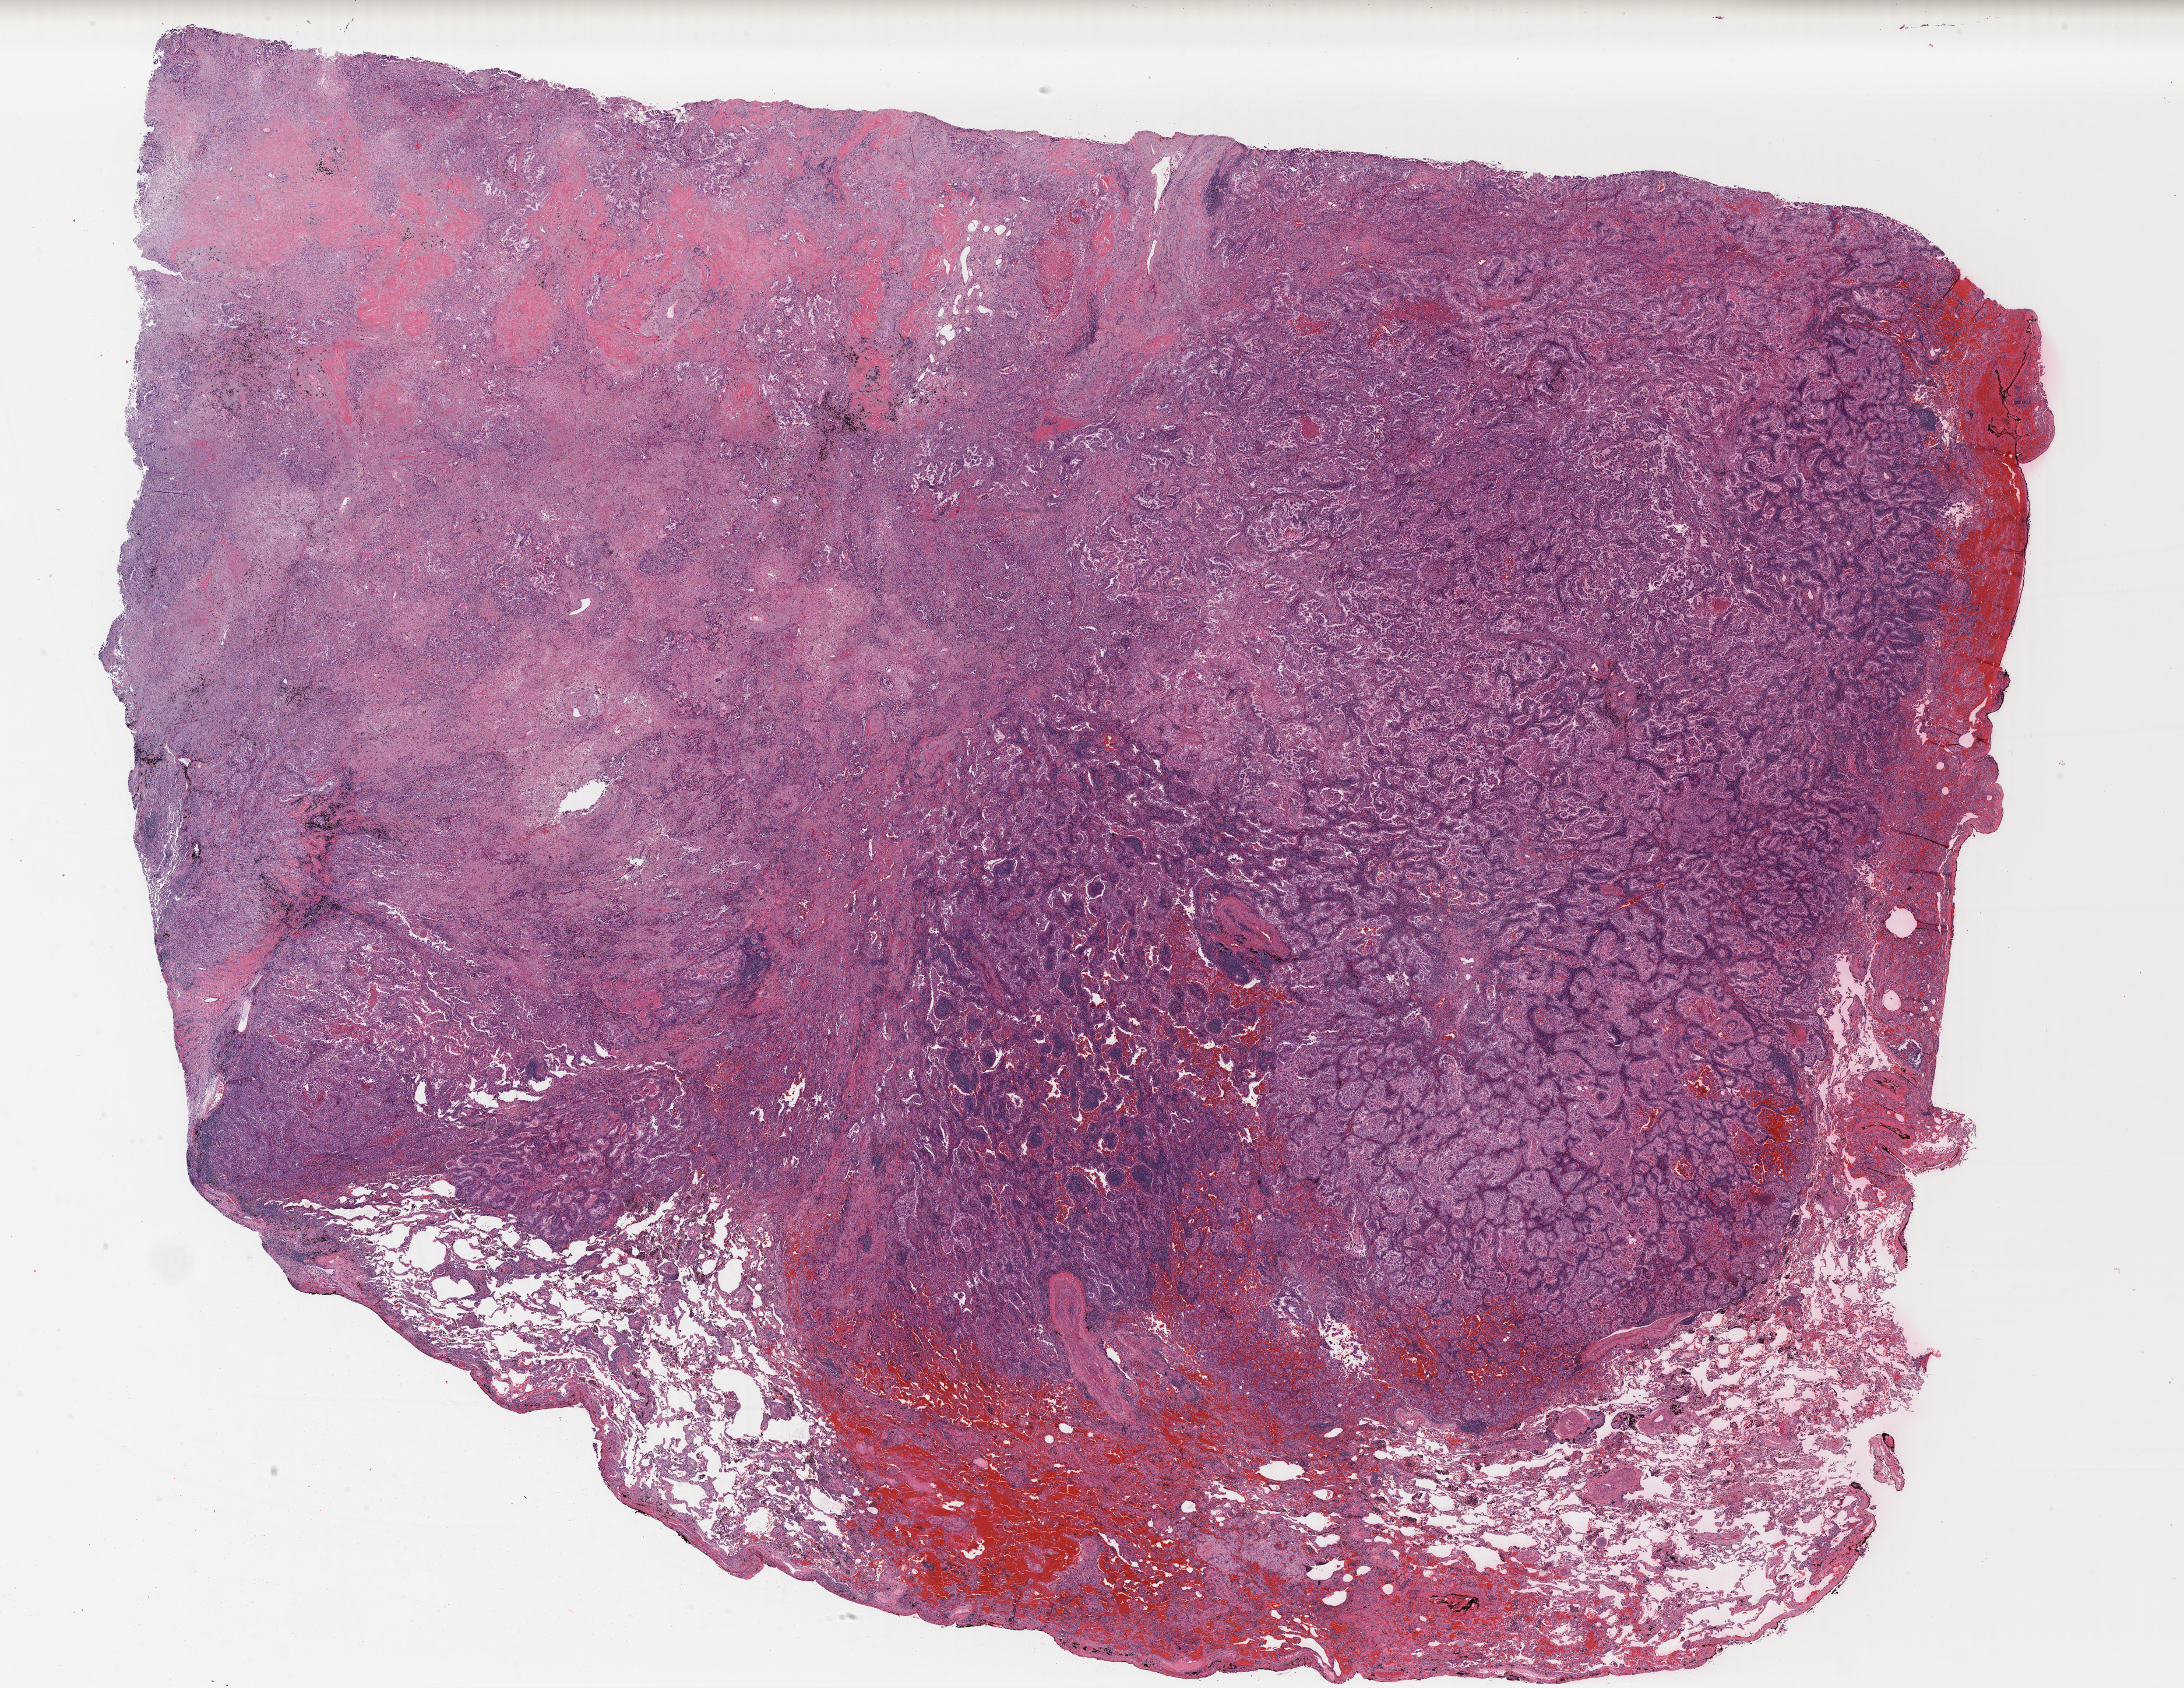
Whole-slide histology image, H&E-stained, low-resolution overview of the scanned area, about 29.5 x 22.8 mm. Formalin-fixed paraffin-embedded (FFPE) diagnostic section. Sample: primary tumour, lung. Female patient; age at initial diagnosis 83 years.
Laterality: left. AJCC pathologic stage: IIIA (7th edition). Histologic diagnosis: Papillary adenocarcinoma, NOS (lower lobe, lung).